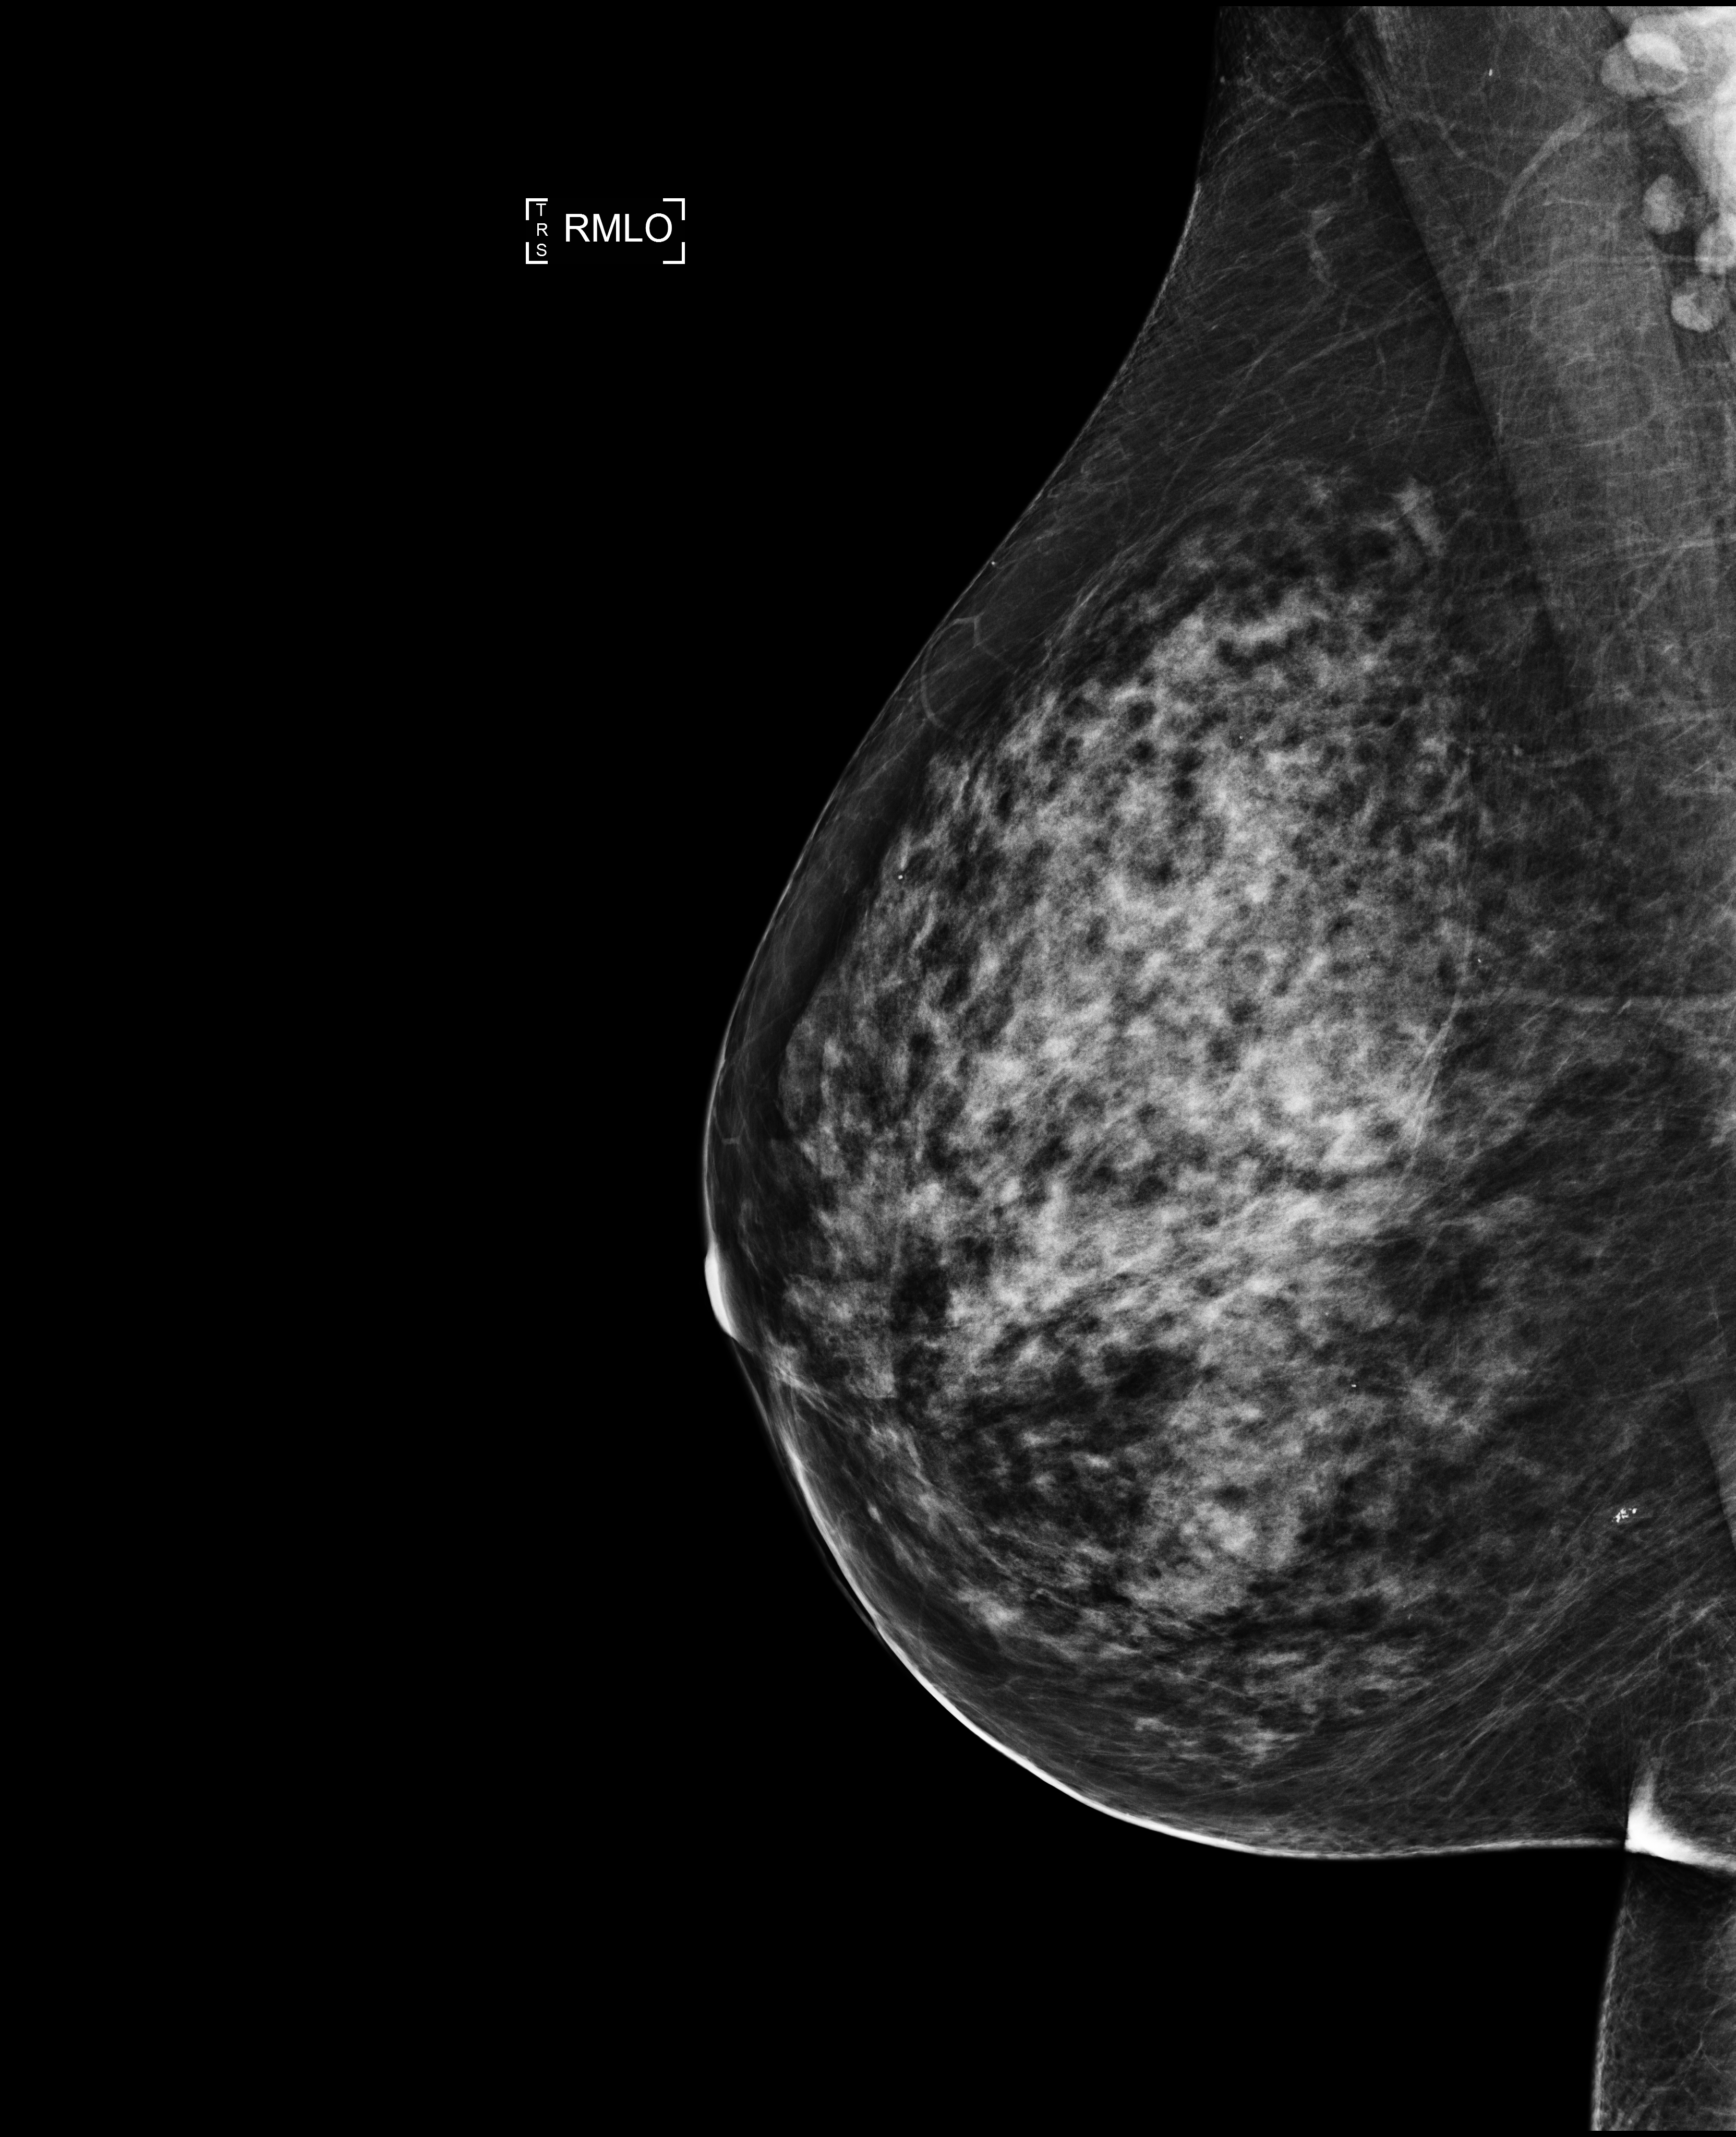
Screening examination. Female patient, age 63 years.
Image type: full-field digital mammogram. Breast: right. Projection: medio-lateral oblique projection.